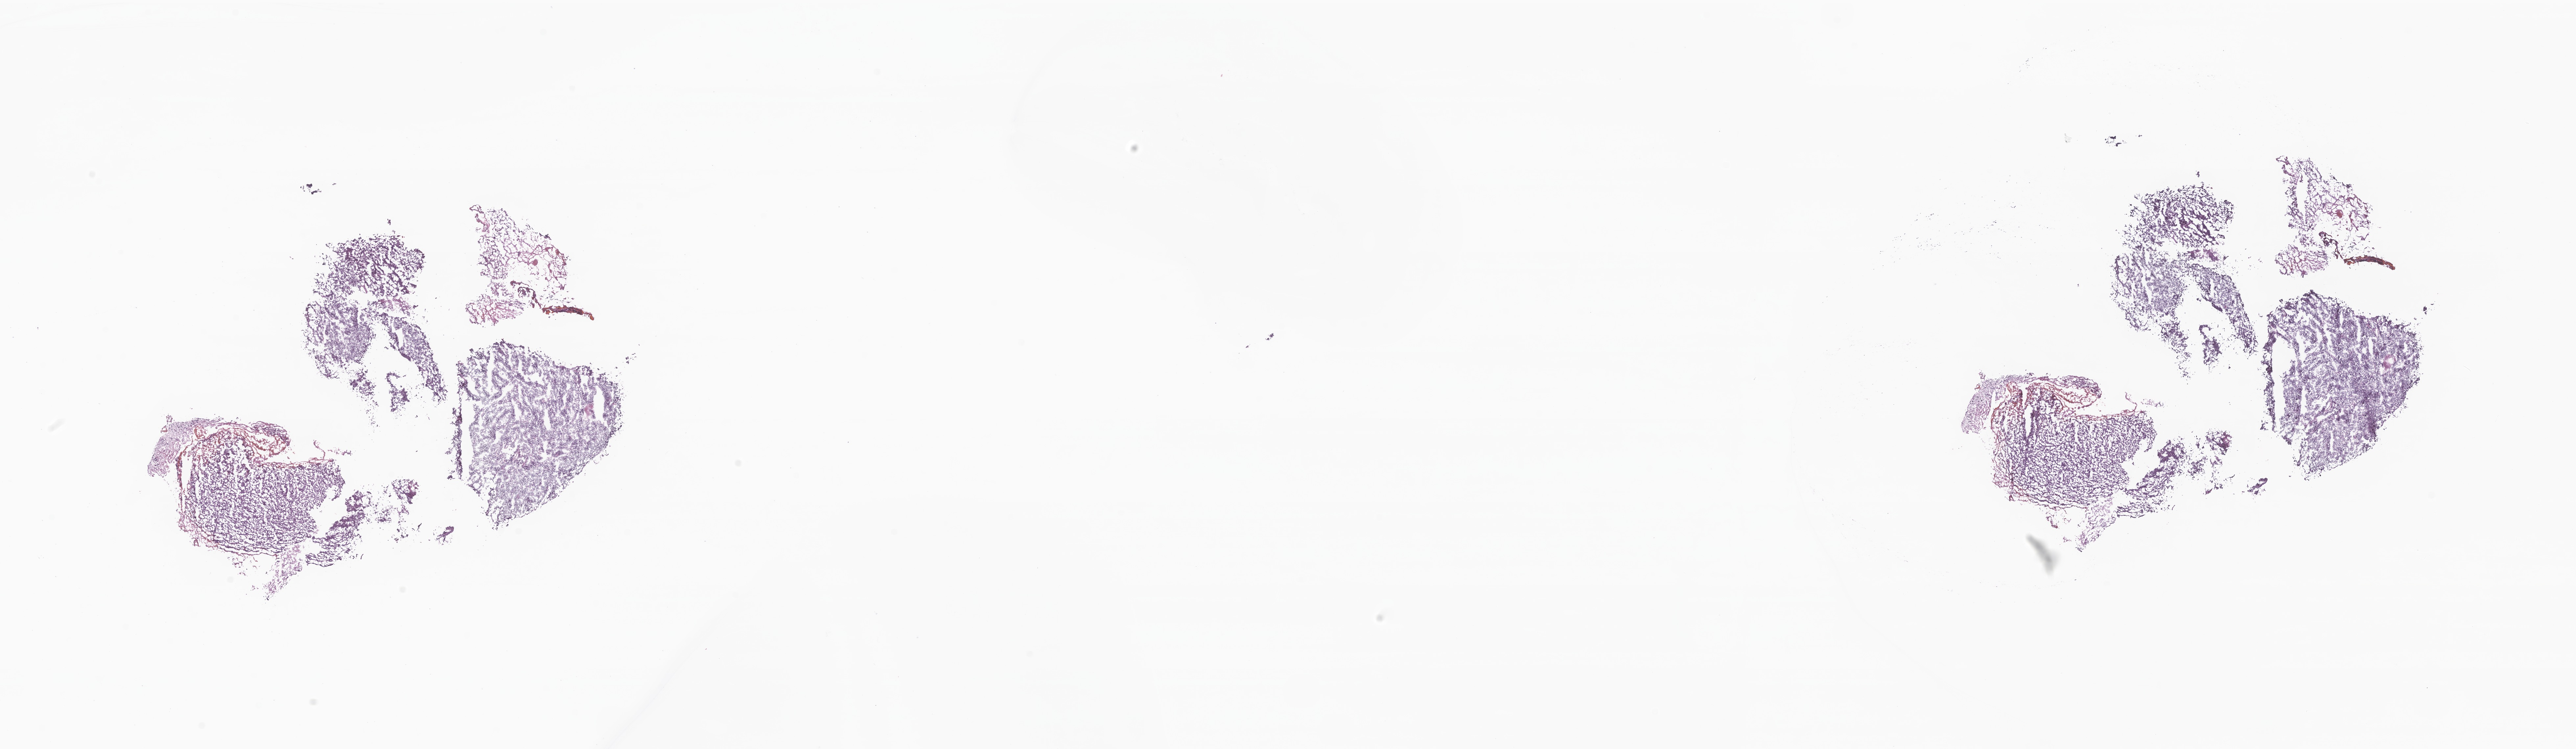
Whole-slide image, H&E stain of tumor tissue from the brain — low-resolution overview of the scanned area, about 33.0 x 9.6 mm. Cryosection (OCT / tissue freezing medium). Patient: female, age 55 months (4 years 7 months).
- recorded diagnosis: Medulloblastoma, NOS